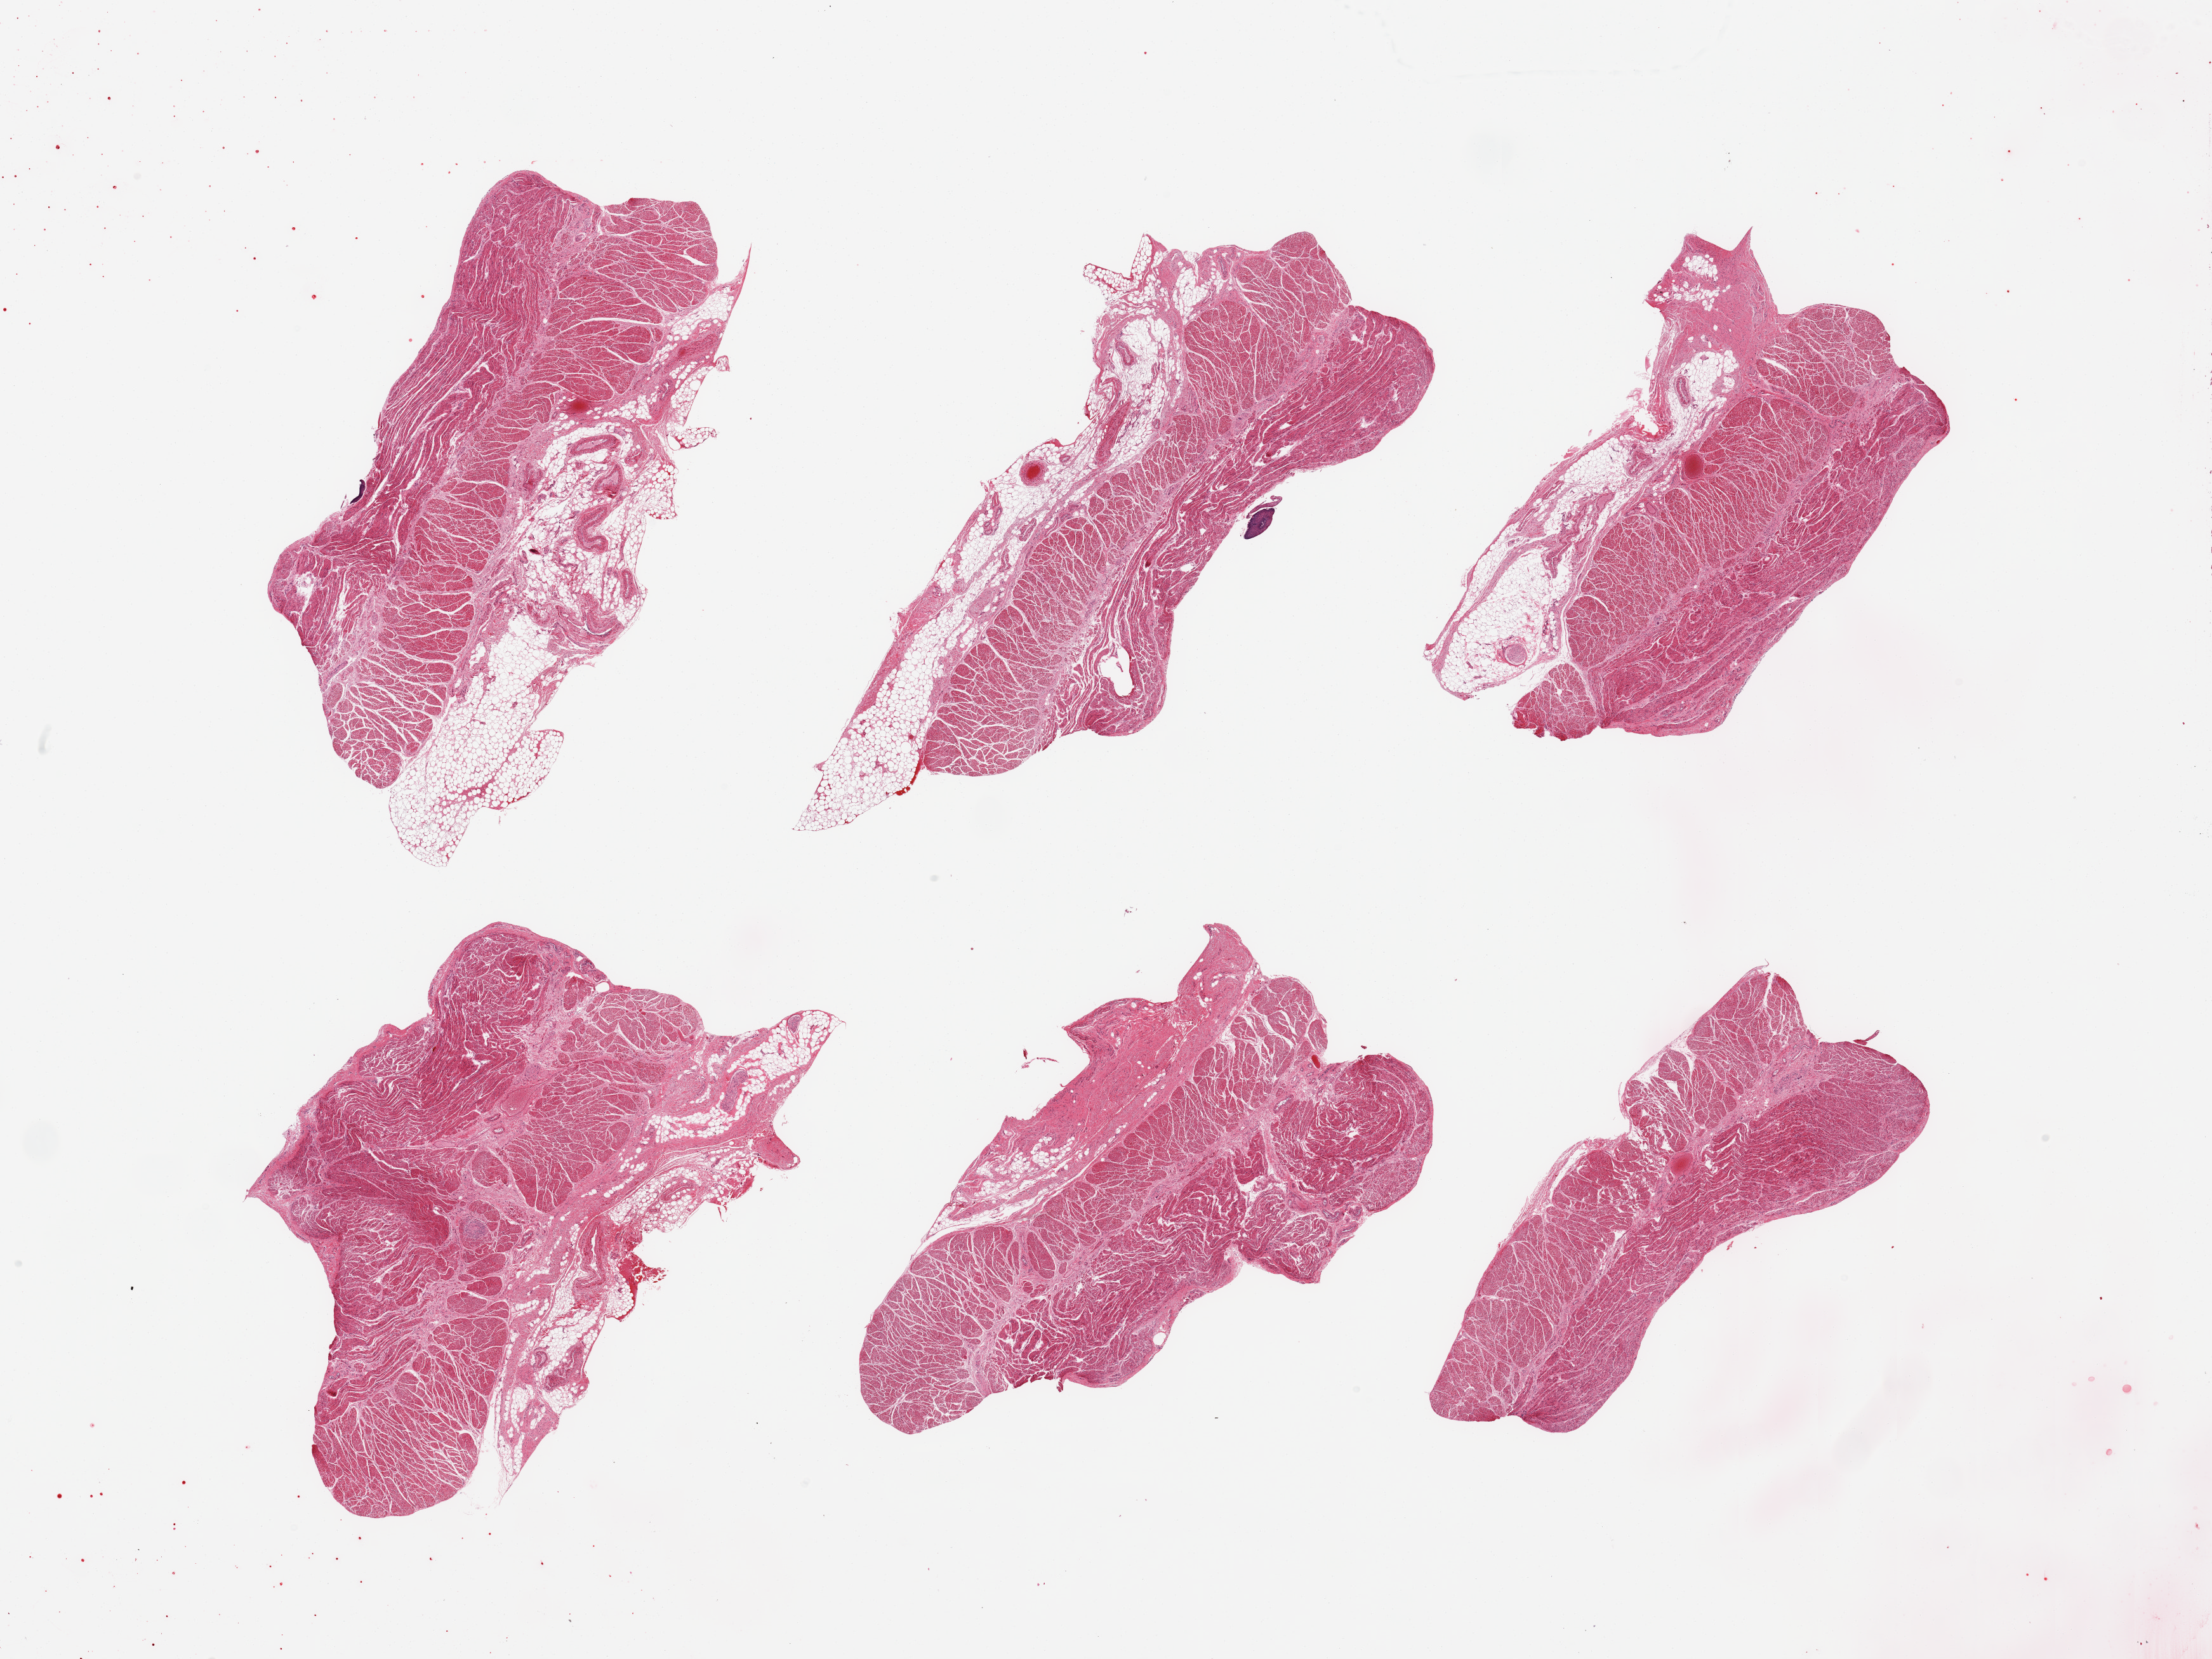
Digitized H&E-stained section, low-resolution overview of the scanned area, about 27.6 x 20.7 mm (acquisition: 20x scan). PAXgene-fixed paraffin-embedded (PFPE) section. Sampled site (target tissue): gastroesophageal junction. Donor tissue sample. Donor: male.
Reviewer comment on this tissue sample: 6 pieces, confirmed target muscularis; Adherent fat up to ~1mm.